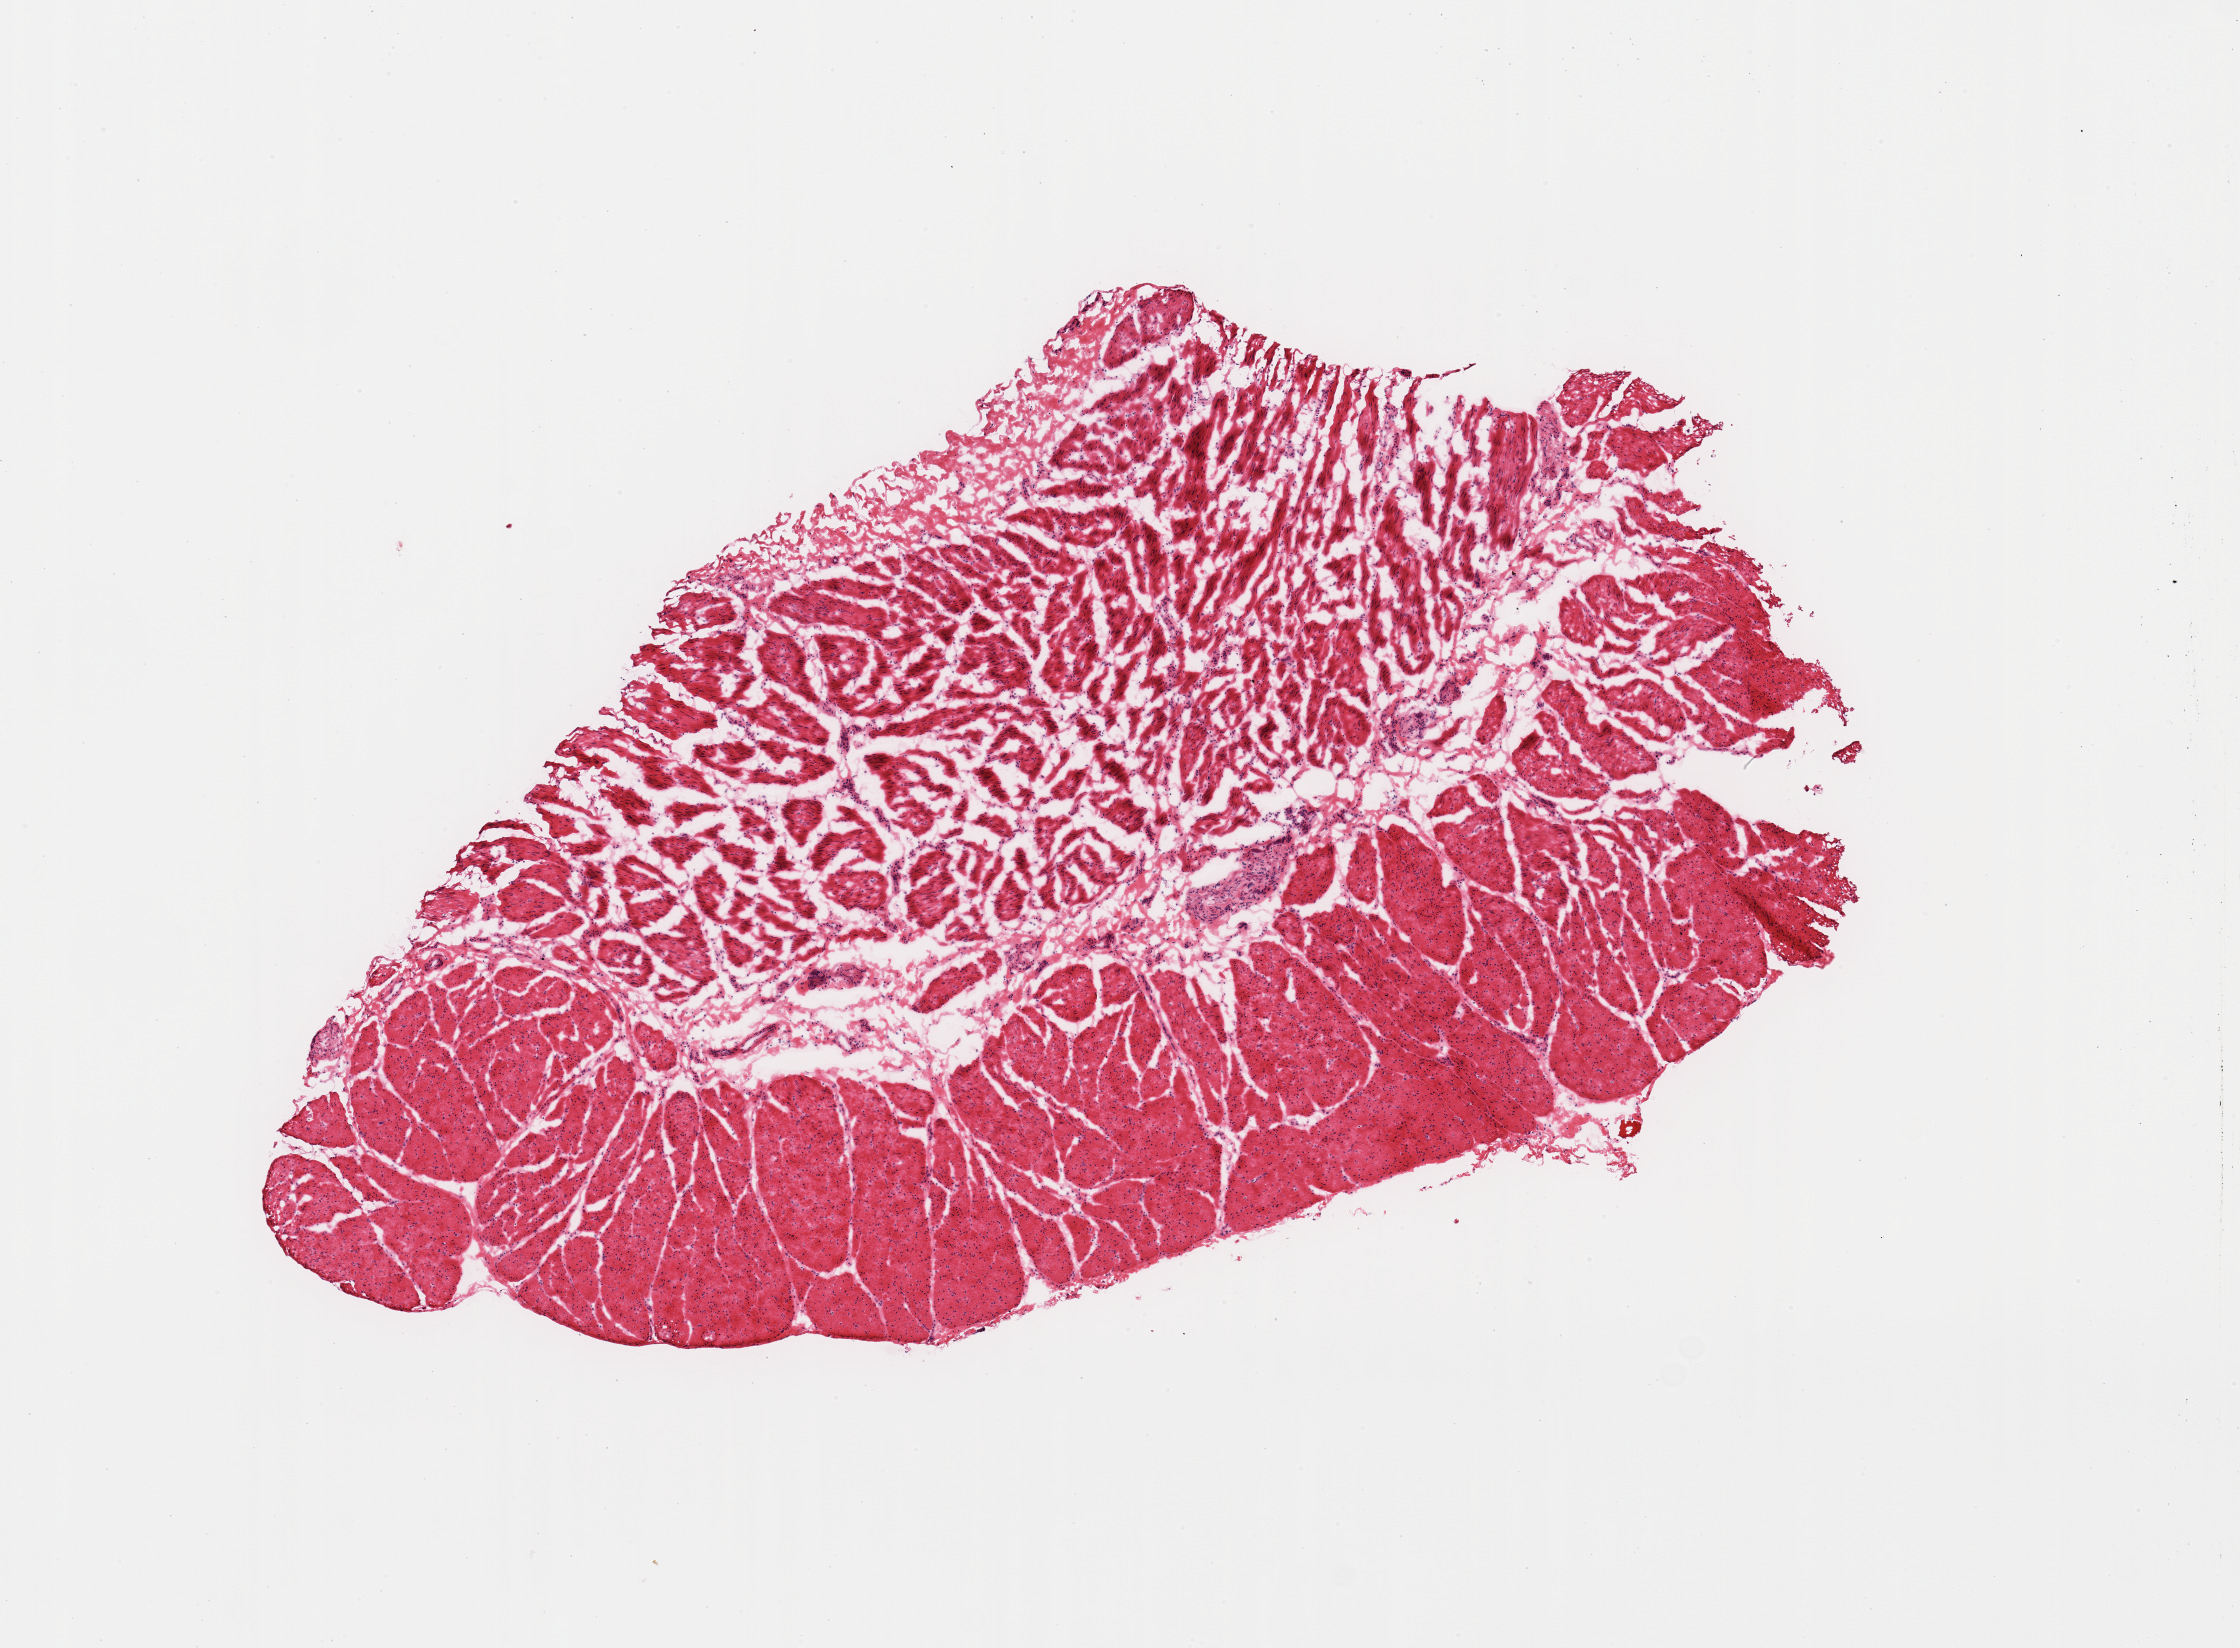
H&E whole-slide image, brightfield — whole scanned area (about 8.9 x 6.5 mm, slide scanned at 20x) shown as a low-resolution overview, frozen section (dry ice), target tissue: esophageal muscle, donor tissue sample. Donor sex: male.
Reviewer comment on this tissue sample: 1 piece.